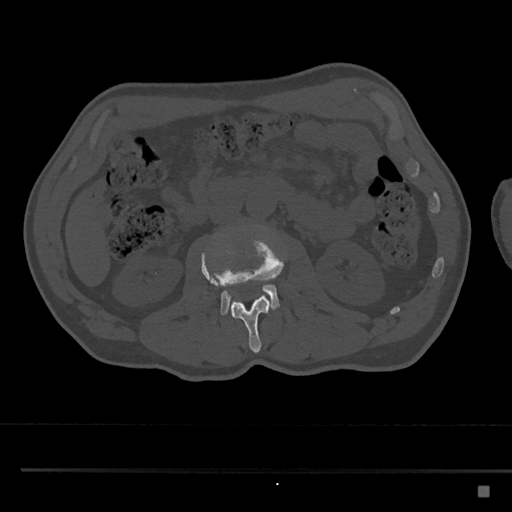
CT including the spine, one axial slice; slice 736 of 797 in the series (ordered by position); 120 kVp; bone window (W 1800 / L 400 HU); 0.5 mm slice thickness; 512 × 512 image matrix, field of view 391 × 391 mm. Male patient, age 59 years. From the clinical record (not read from this slice): primary cancer: prostate.
Structures marked on this image (semi-automatic segmentation, software-assisted and operator-edited):
- L2 vertebra: bounding box (x1, y1, x2, y2) in pixels: (201, 235, 283, 353)
- L3 vertebra: (201, 261, 280, 316)